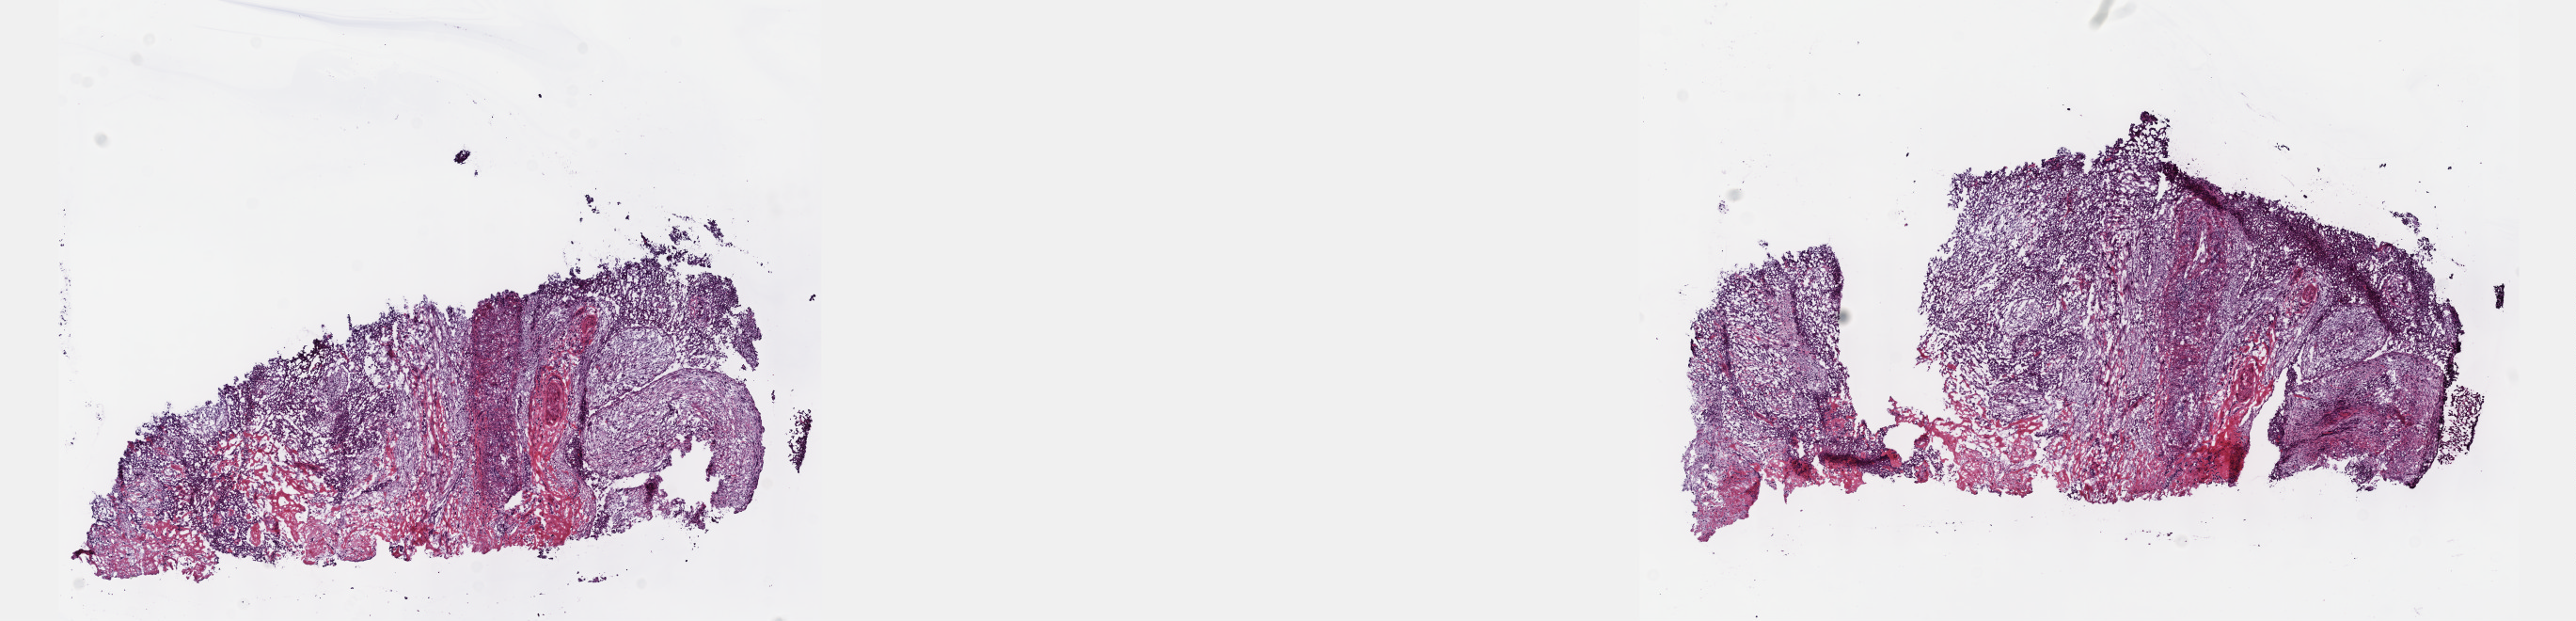
Whole-slide histology image, H&E, shown as a low-resolution overview of the whole scanned area (about 22.1 x 5.3 mm, from a 40x scan); frozen section from the top of the tissue portion; bladder, primary tumour sample. Male patient. Histologic grade: high grade. Composition of this section per pathologist review: tumour cells 100%, tumour nuclei 65%, normal cells 0%, stromal cells 0%, necrosis 0%. Infiltration values recorded for this section: lymphocyte infiltration 3%, monocyte infiltration 0%, neutrophil infiltration 0%.
Diagnosis: Transitional cell carcinoma. TNM: T4 N1 MX. AJCC pathologic stage: IV (6th edition).